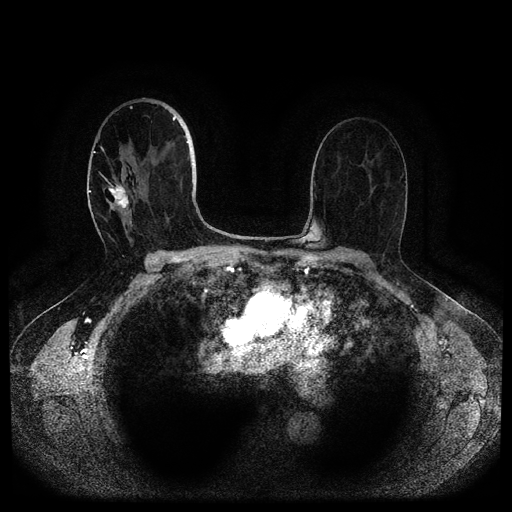
Breast MRI (dynamic contrast-enhanced, multi-phase), one axial slice; position 62 of 116 along the scan axis; dynamic contrast-enhanced series, time point 2 of 5 at this slice position (early post-contrast); 1.5 T; TE 2.6 ms, TR 5.3 ms; 2 mm slice thickness; 512 × 512 image matrix. Patient: female, 82 years.
Structures marked on this image (semi-automatic segmentation, software-assisted and operator-edited):
- breast lesion (labelled 'tumour' in the annotation; benign lesions carry a separate 'benign' label): bounding box [x1, y1, x2, y2] px = [108, 180, 132, 213]